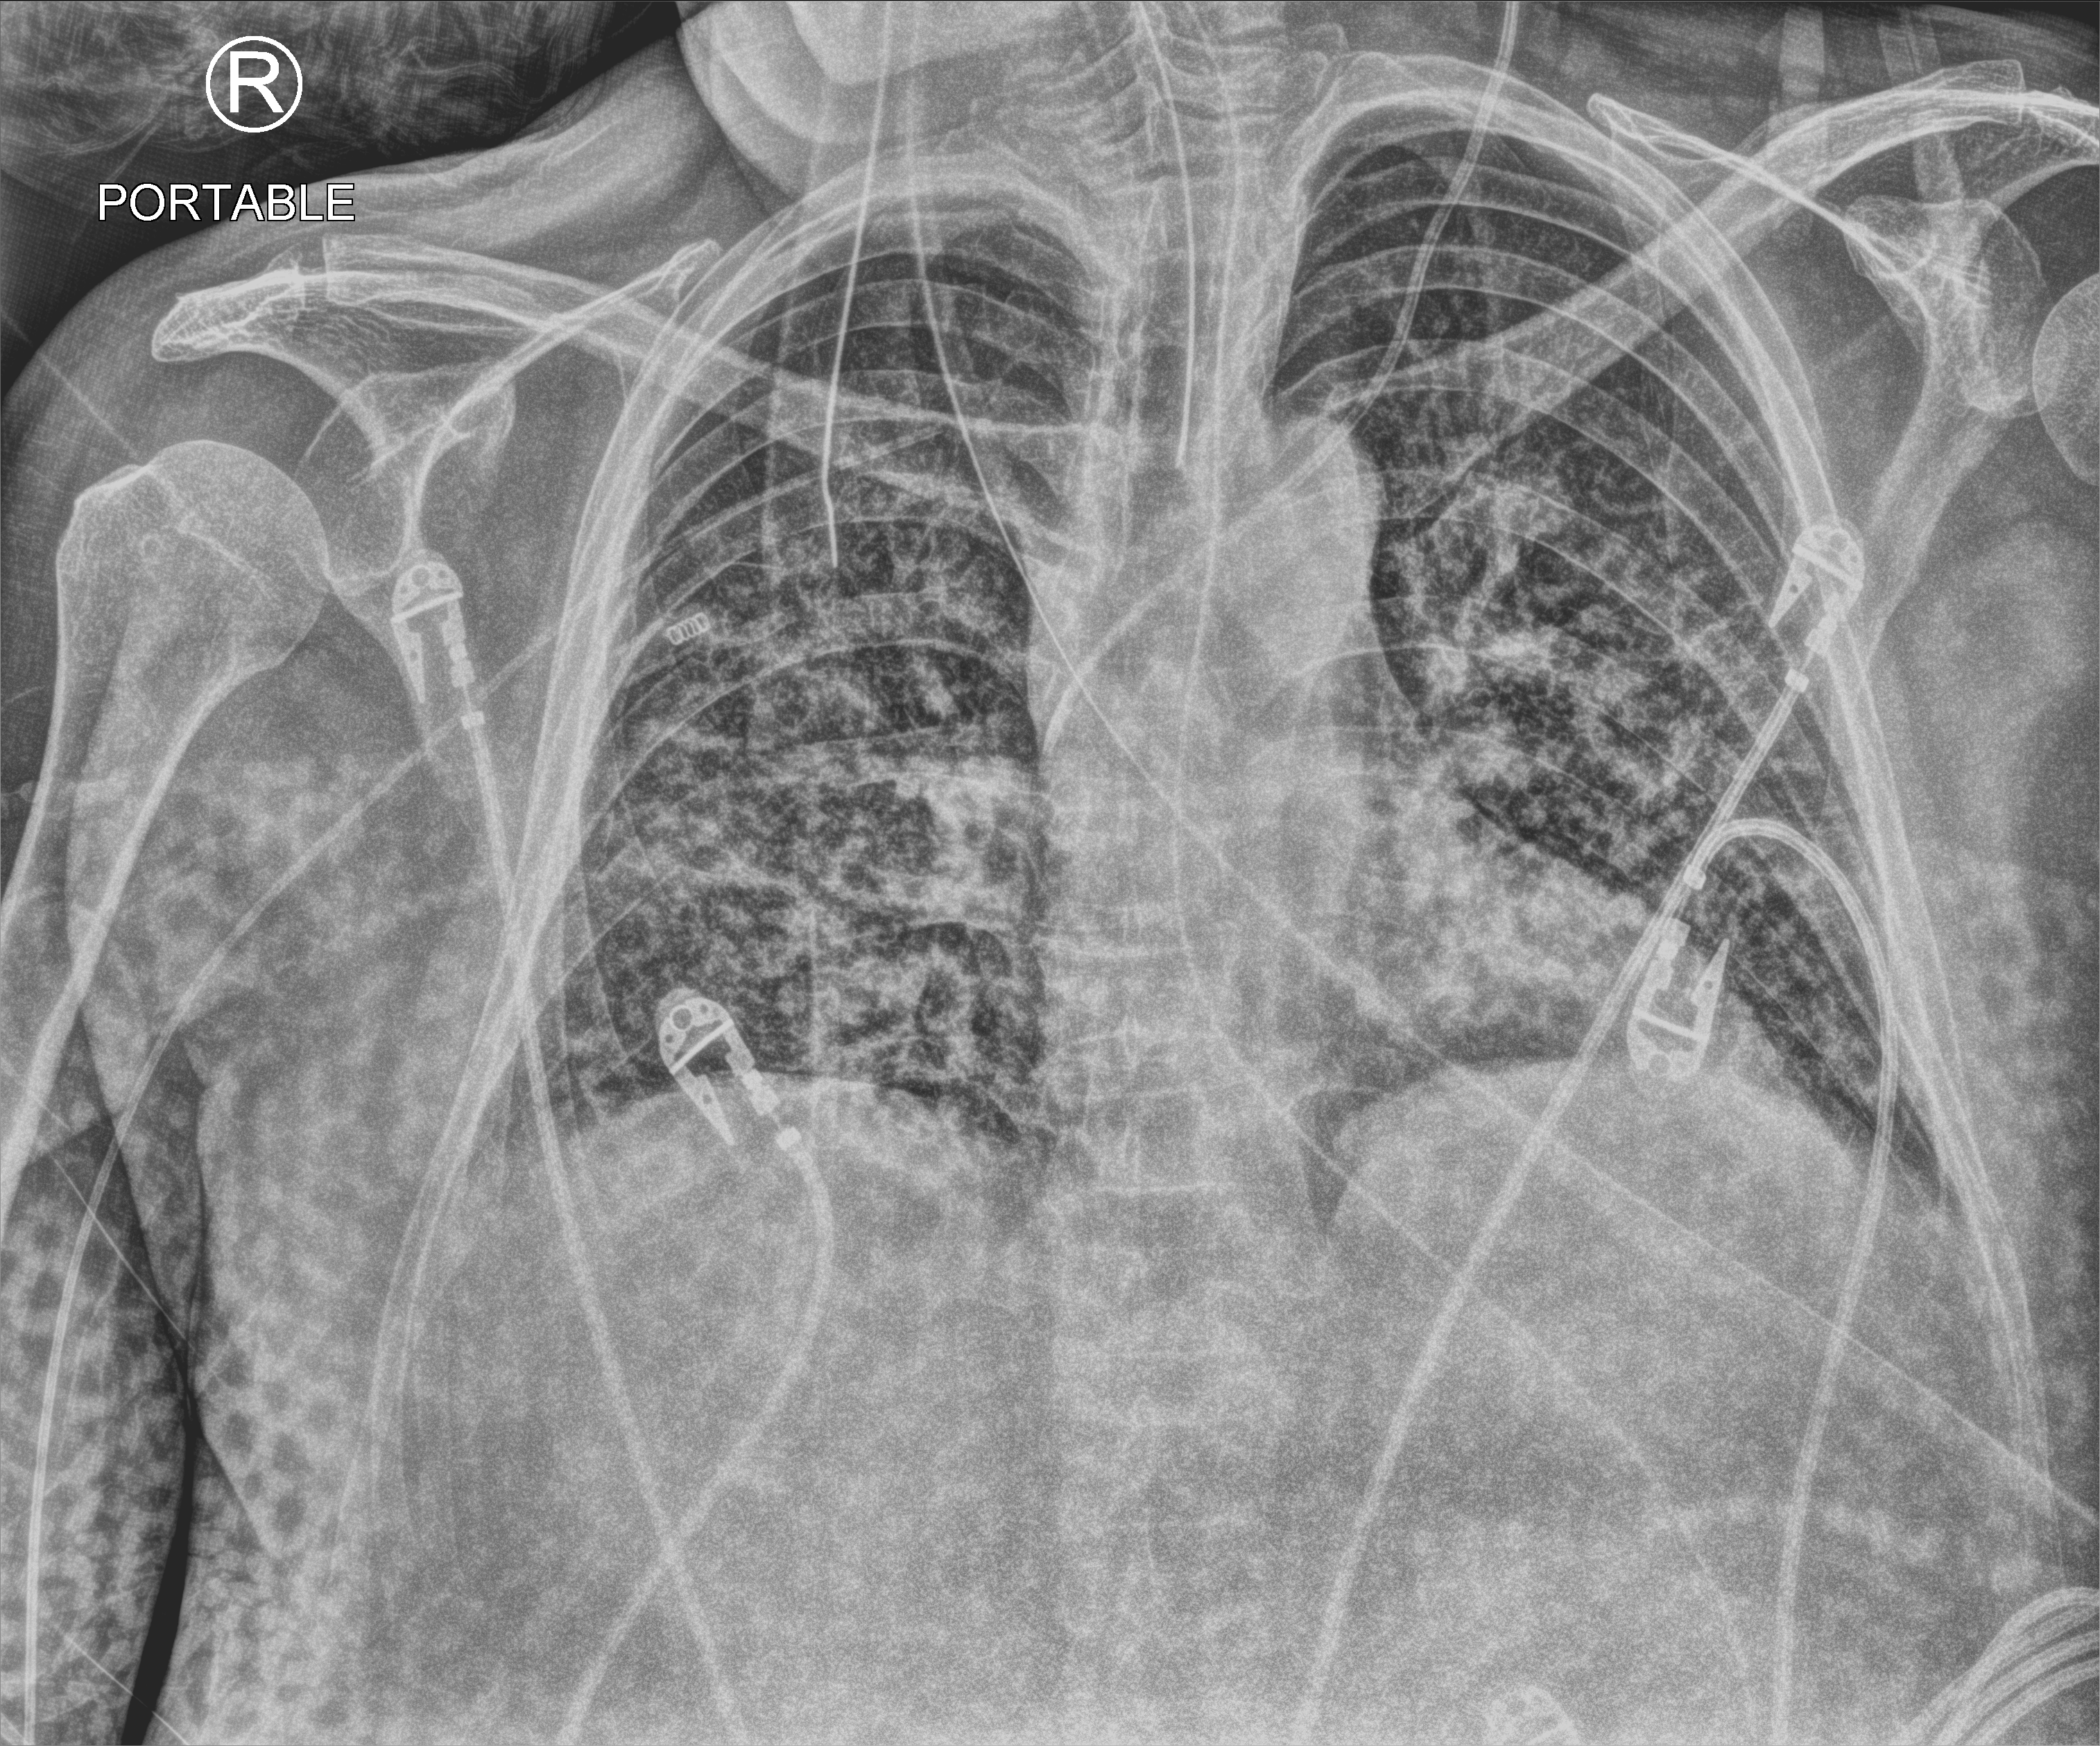
Chest X-ray (portable); anteroposterior (AP) projection. Patient hospitalised with COVID-19; male, aged 60–74 years.
Admission-level facts for this patient (not findings on this image; timing relative to this image not recorded): chronic kidney disease (admission record): no.